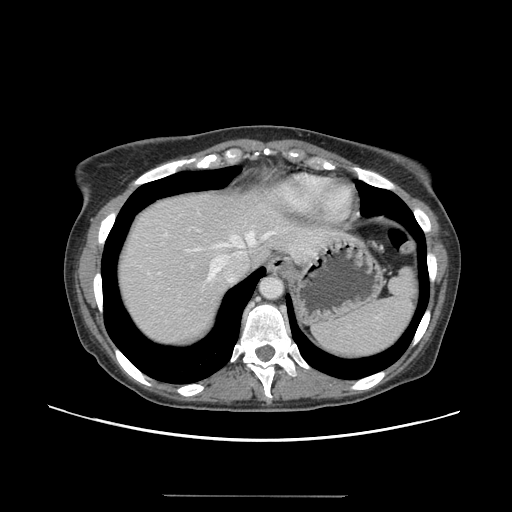
Contrast-enhanced abdominal CT, one axial slice; slice 123 of 144 in the series (ordered by position); 120 kVp; intravenous contrast given; soft-tissue window (W 400 / L 40 HU); 2.5 mm slice thickness; 512 × 512 image matrix, field of view 380 × 380 mm. Female patient, age 53 years. From the clinical record (not read from this slice): diagnosis: colorectal cancer liver metastases, imaged before liver resection; multiple liver metastases: yes; largest metastasis: 1.1 cm.
Structures marked on this image (expert manual segmentation):
- hepatic veins: bounding box <195,232,274,281> (left, top, right, bottom; pixels)
- liver: <118,188,319,345>
- planned liver remnant (the part of the liver to remain after resection): <118,186,271,296>